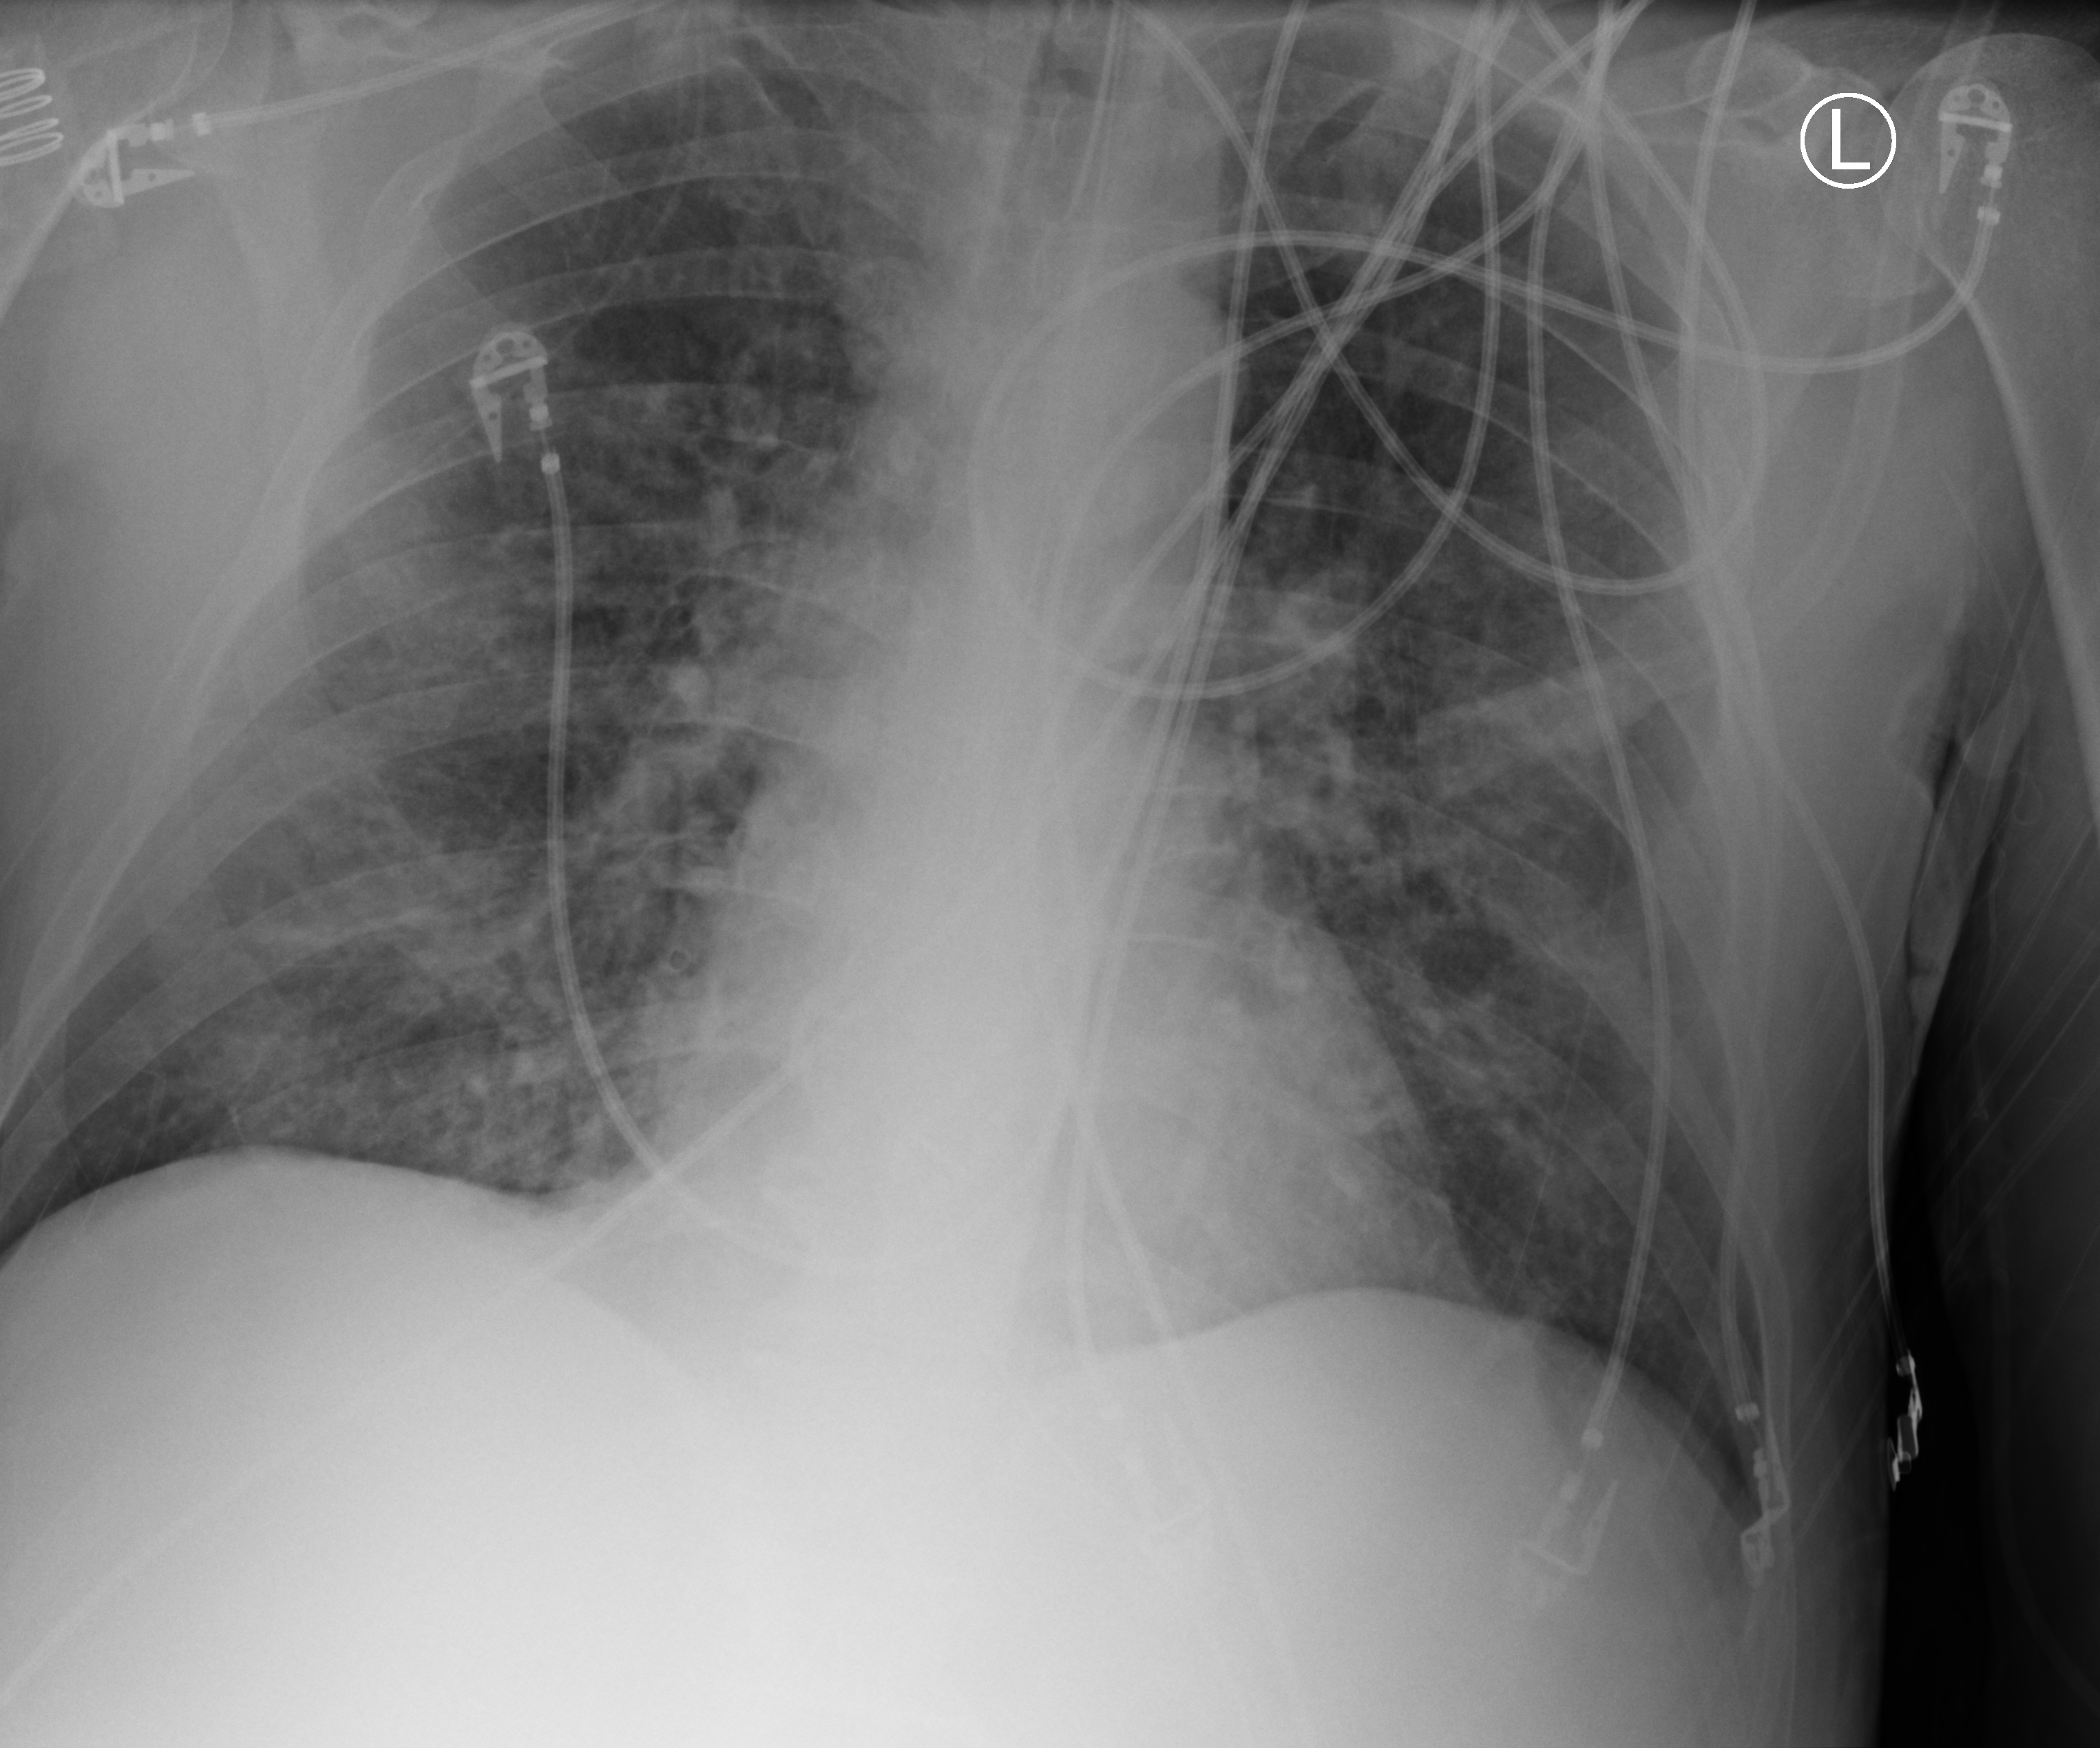
Bedside chest radiograph (computed radiography), anteroposterior (AP) projection. Patient hospitalised with COVID-19; male, aged 18–59 years.
Admission-level facts for this patient (not findings on this image; timing relative to this image not recorded): admitted to intensive care during this hospital stay: no; length of hospital stay: 19 days; diabetes (admission record): no.